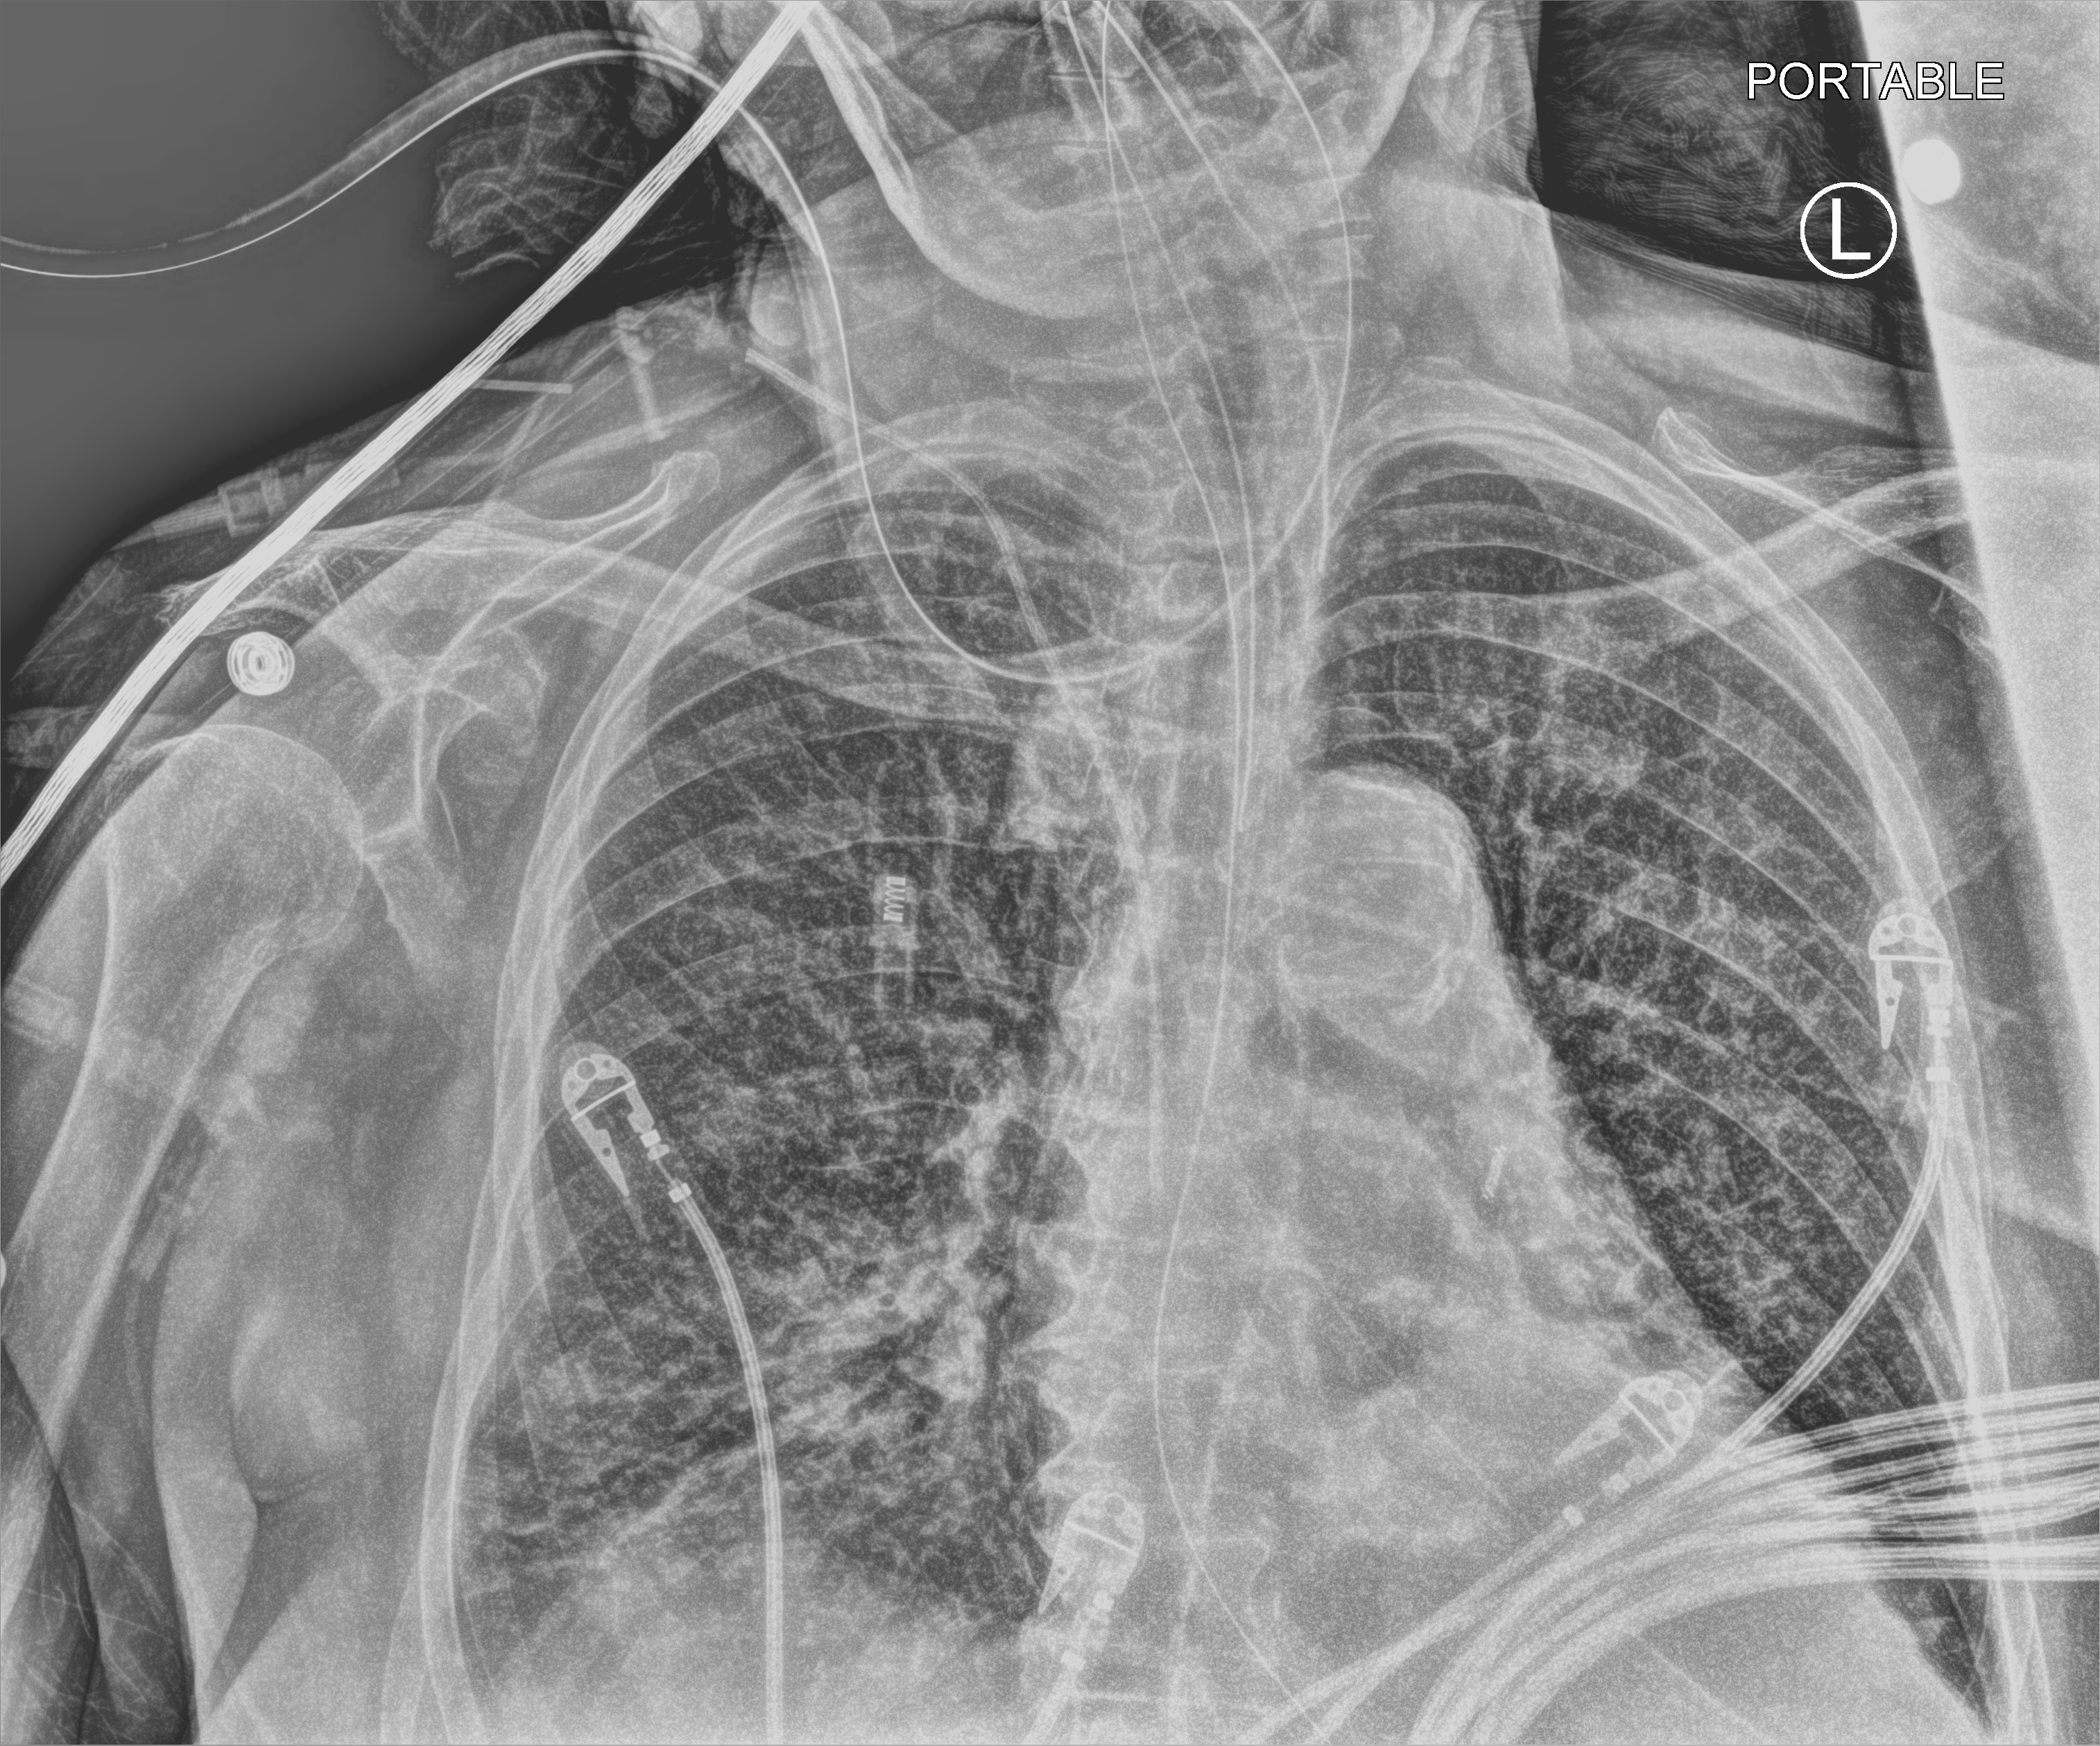
Portable chest radiograph, anteroposterior (AP) projection. Female patient hospitalised with COVID-19, age 75–90 years.
Admission-level facts for this patient (not findings on this image; timing relative to this image not recorded):
- chronic kidney disease (admission record): yes
- diabetes (admission record): yes